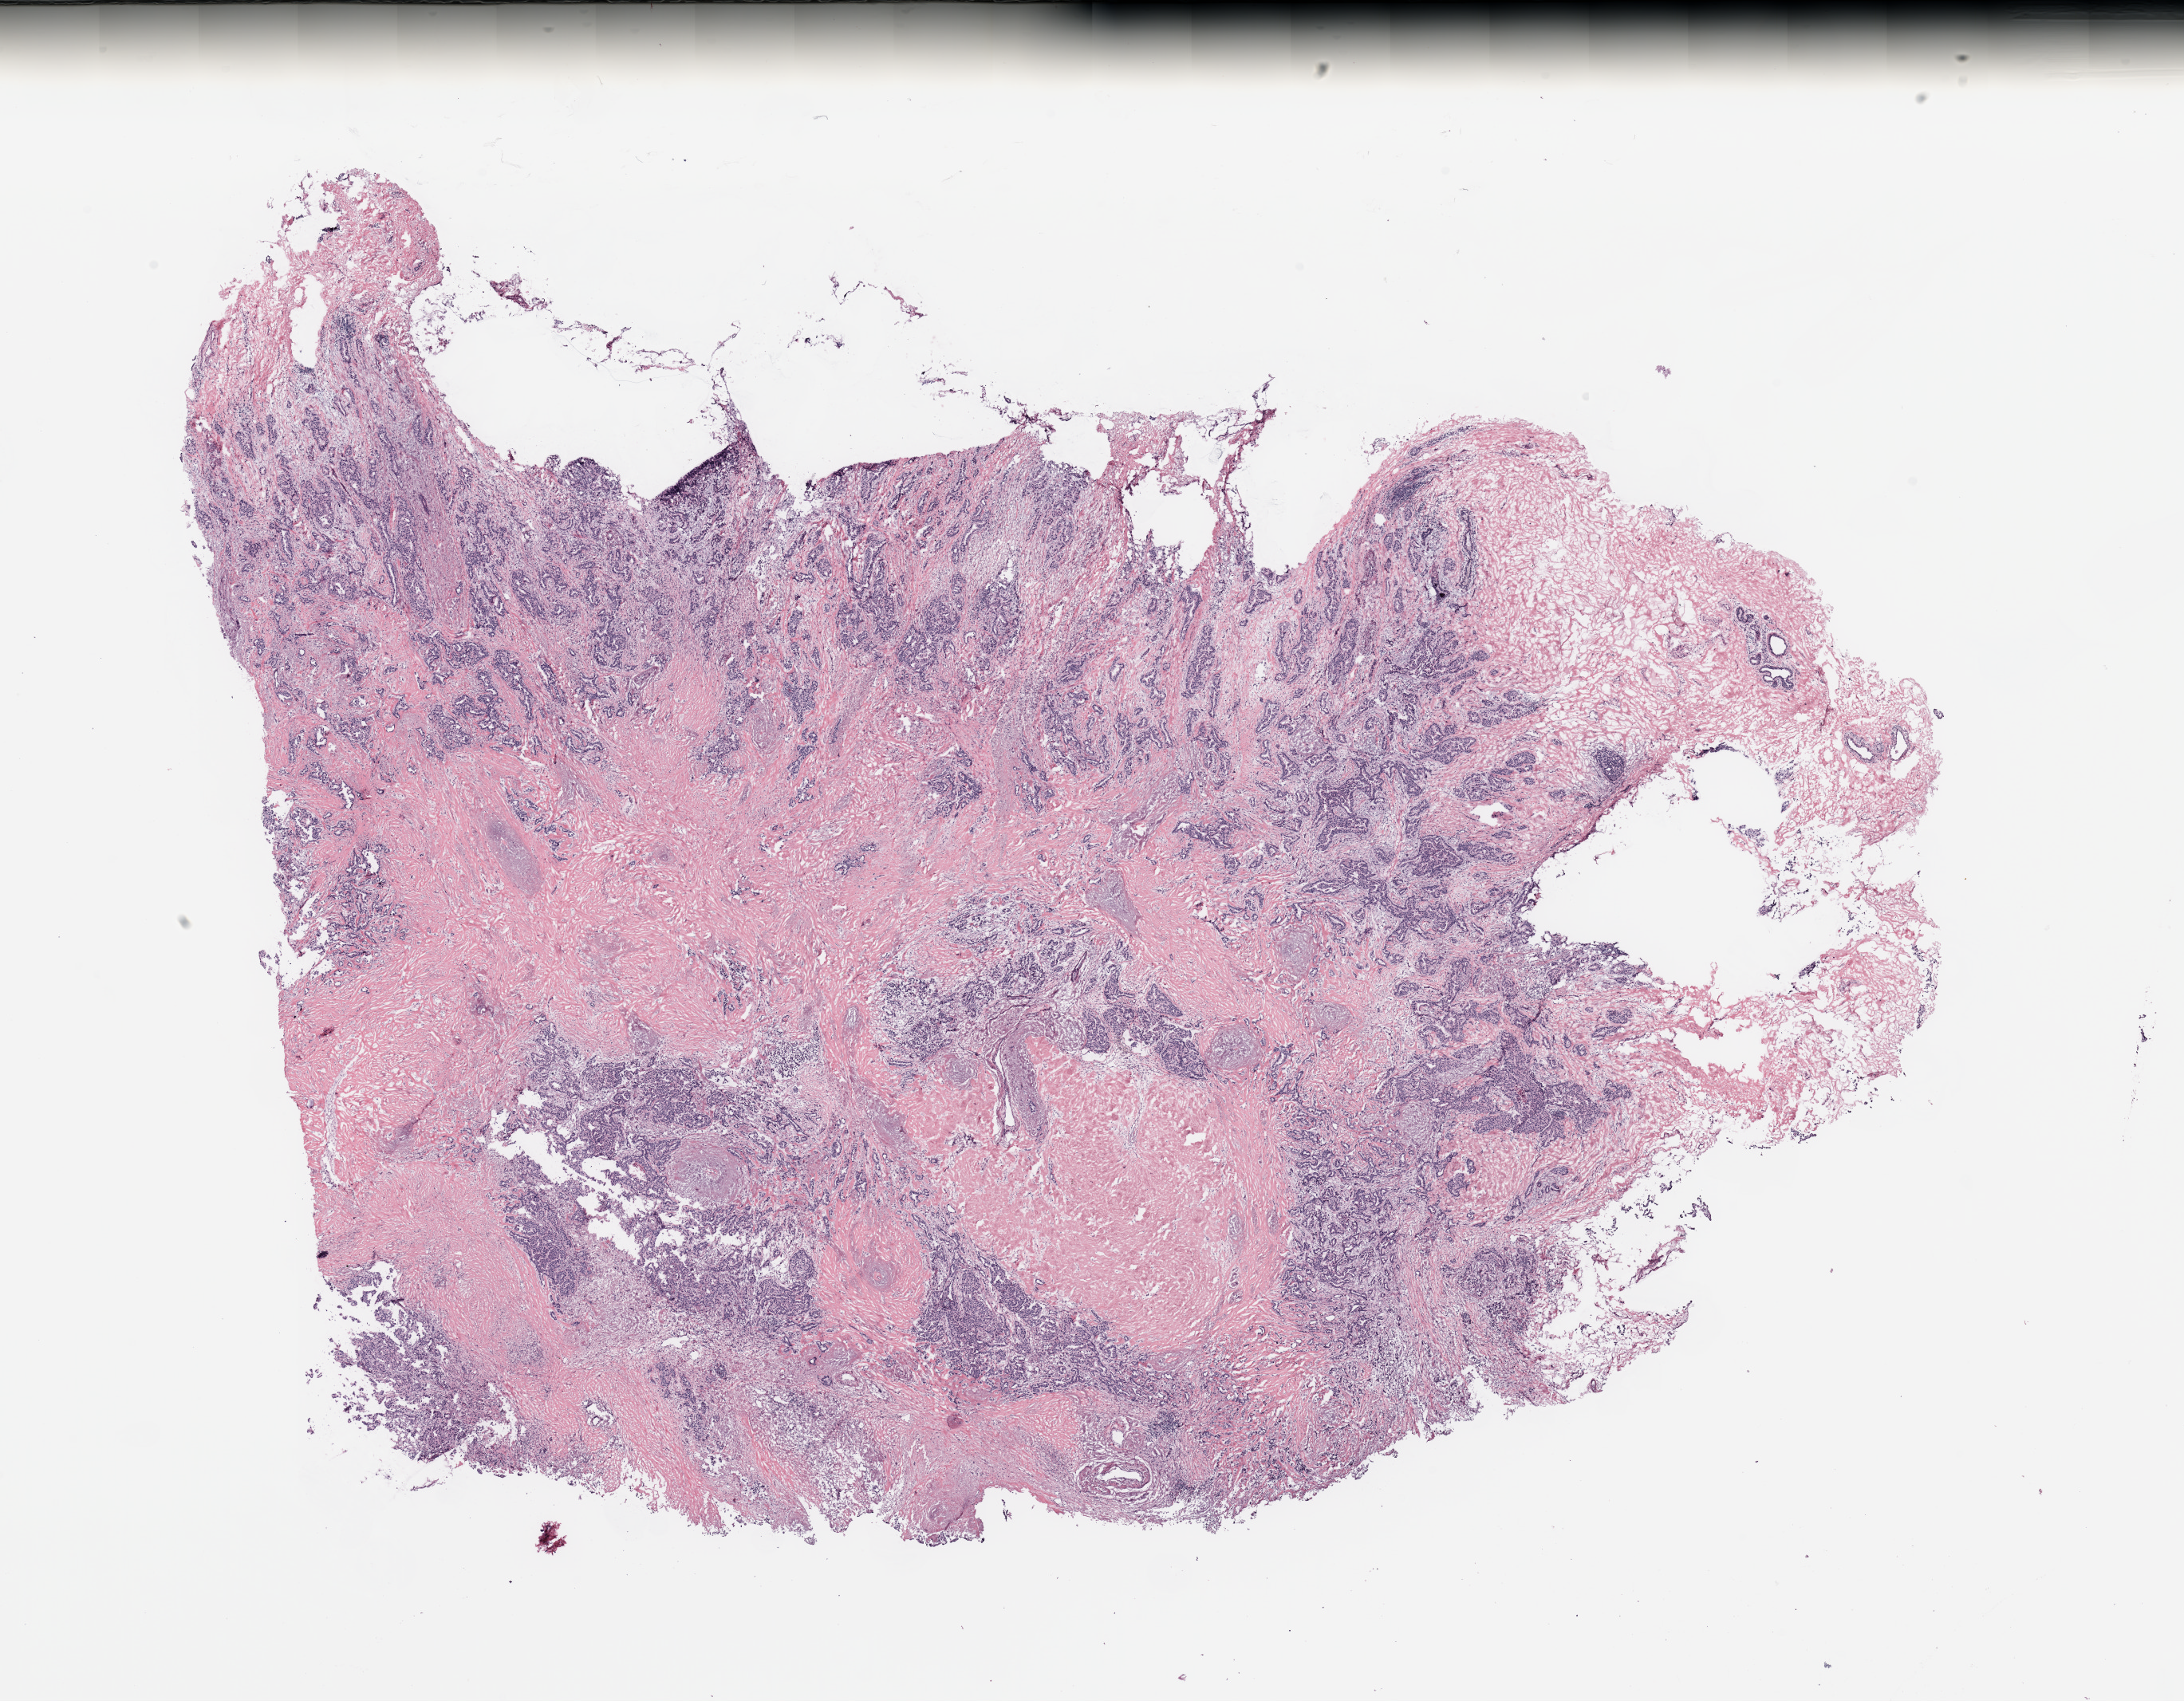
Whole-slide histology image, H&E, low-resolution overview of the scanned area, about 21.7 x 16.9 mm; breast, tissue type not recorded.
* patient diagnosis (cohort enrolment): breast cancer (breast)